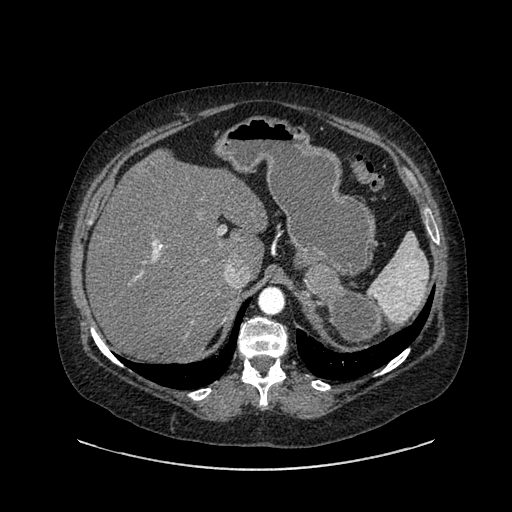
Contrast-enhanced abdominal CT, one axial slice. Position 626 of 769 along the scan axis. Reconstruction kernel SOFT. 120 kVp. Intravenous contrast given. Soft-tissue window (W 400 / L 40 HU). 512 × 512 image matrix, field of view 460 × 460 mm. Patient: female, 61 years. From the clinical record (not read from this slice): diagnosis: adrenocortical carcinoma; tumour side: left adrenal; tumour size at pathology: 13 cm.
Structures marked on this image (semi-automatically segmented with operator editing):
- mass: bounding box (x1, y1, x2, y2) in pixels: (302, 266, 382, 346)